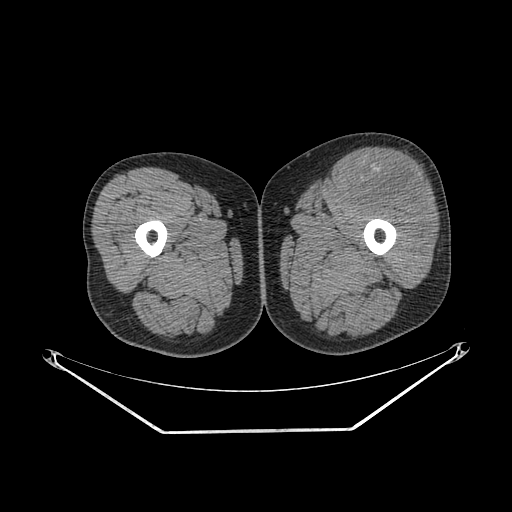
CT of an extremity soft-tissue mass (from a PET/CT study), one axial slice; 140 kVp; soft-tissue window (W 400 / L 40 HU); 512 × 512 image matrix. Male patient. From the clinical record (not read from this slice): histological type: extraskeletal osteosarcoma; grade: high; site of the primary tumour: thigh.
Outlined on this slice (expert contour drawn on MRI and transferred to this co-registered scan by the dataset authors):
- gross tumour volume (mass): bounding box <354,160,430,211> (left, top, right, bottom; pixels)